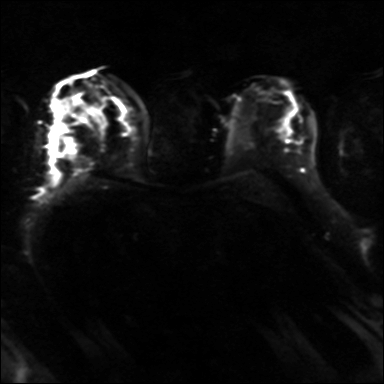
Breast MRI, one axial slice. Position 20 of 36 along the scan axis. Diffusion-weighted series; image 2 of 4 stored at this slice position (different b-values; order by instance number). 3 T. 384 × 384 image matrix, field of view 320 × 320 mm. Female patient.
Outlined on this slice (expert manual segmentation):
- tumour on diffusion-weighted imaging: bounding box <63,134,77,157> (left, top, right, bottom; pixels)